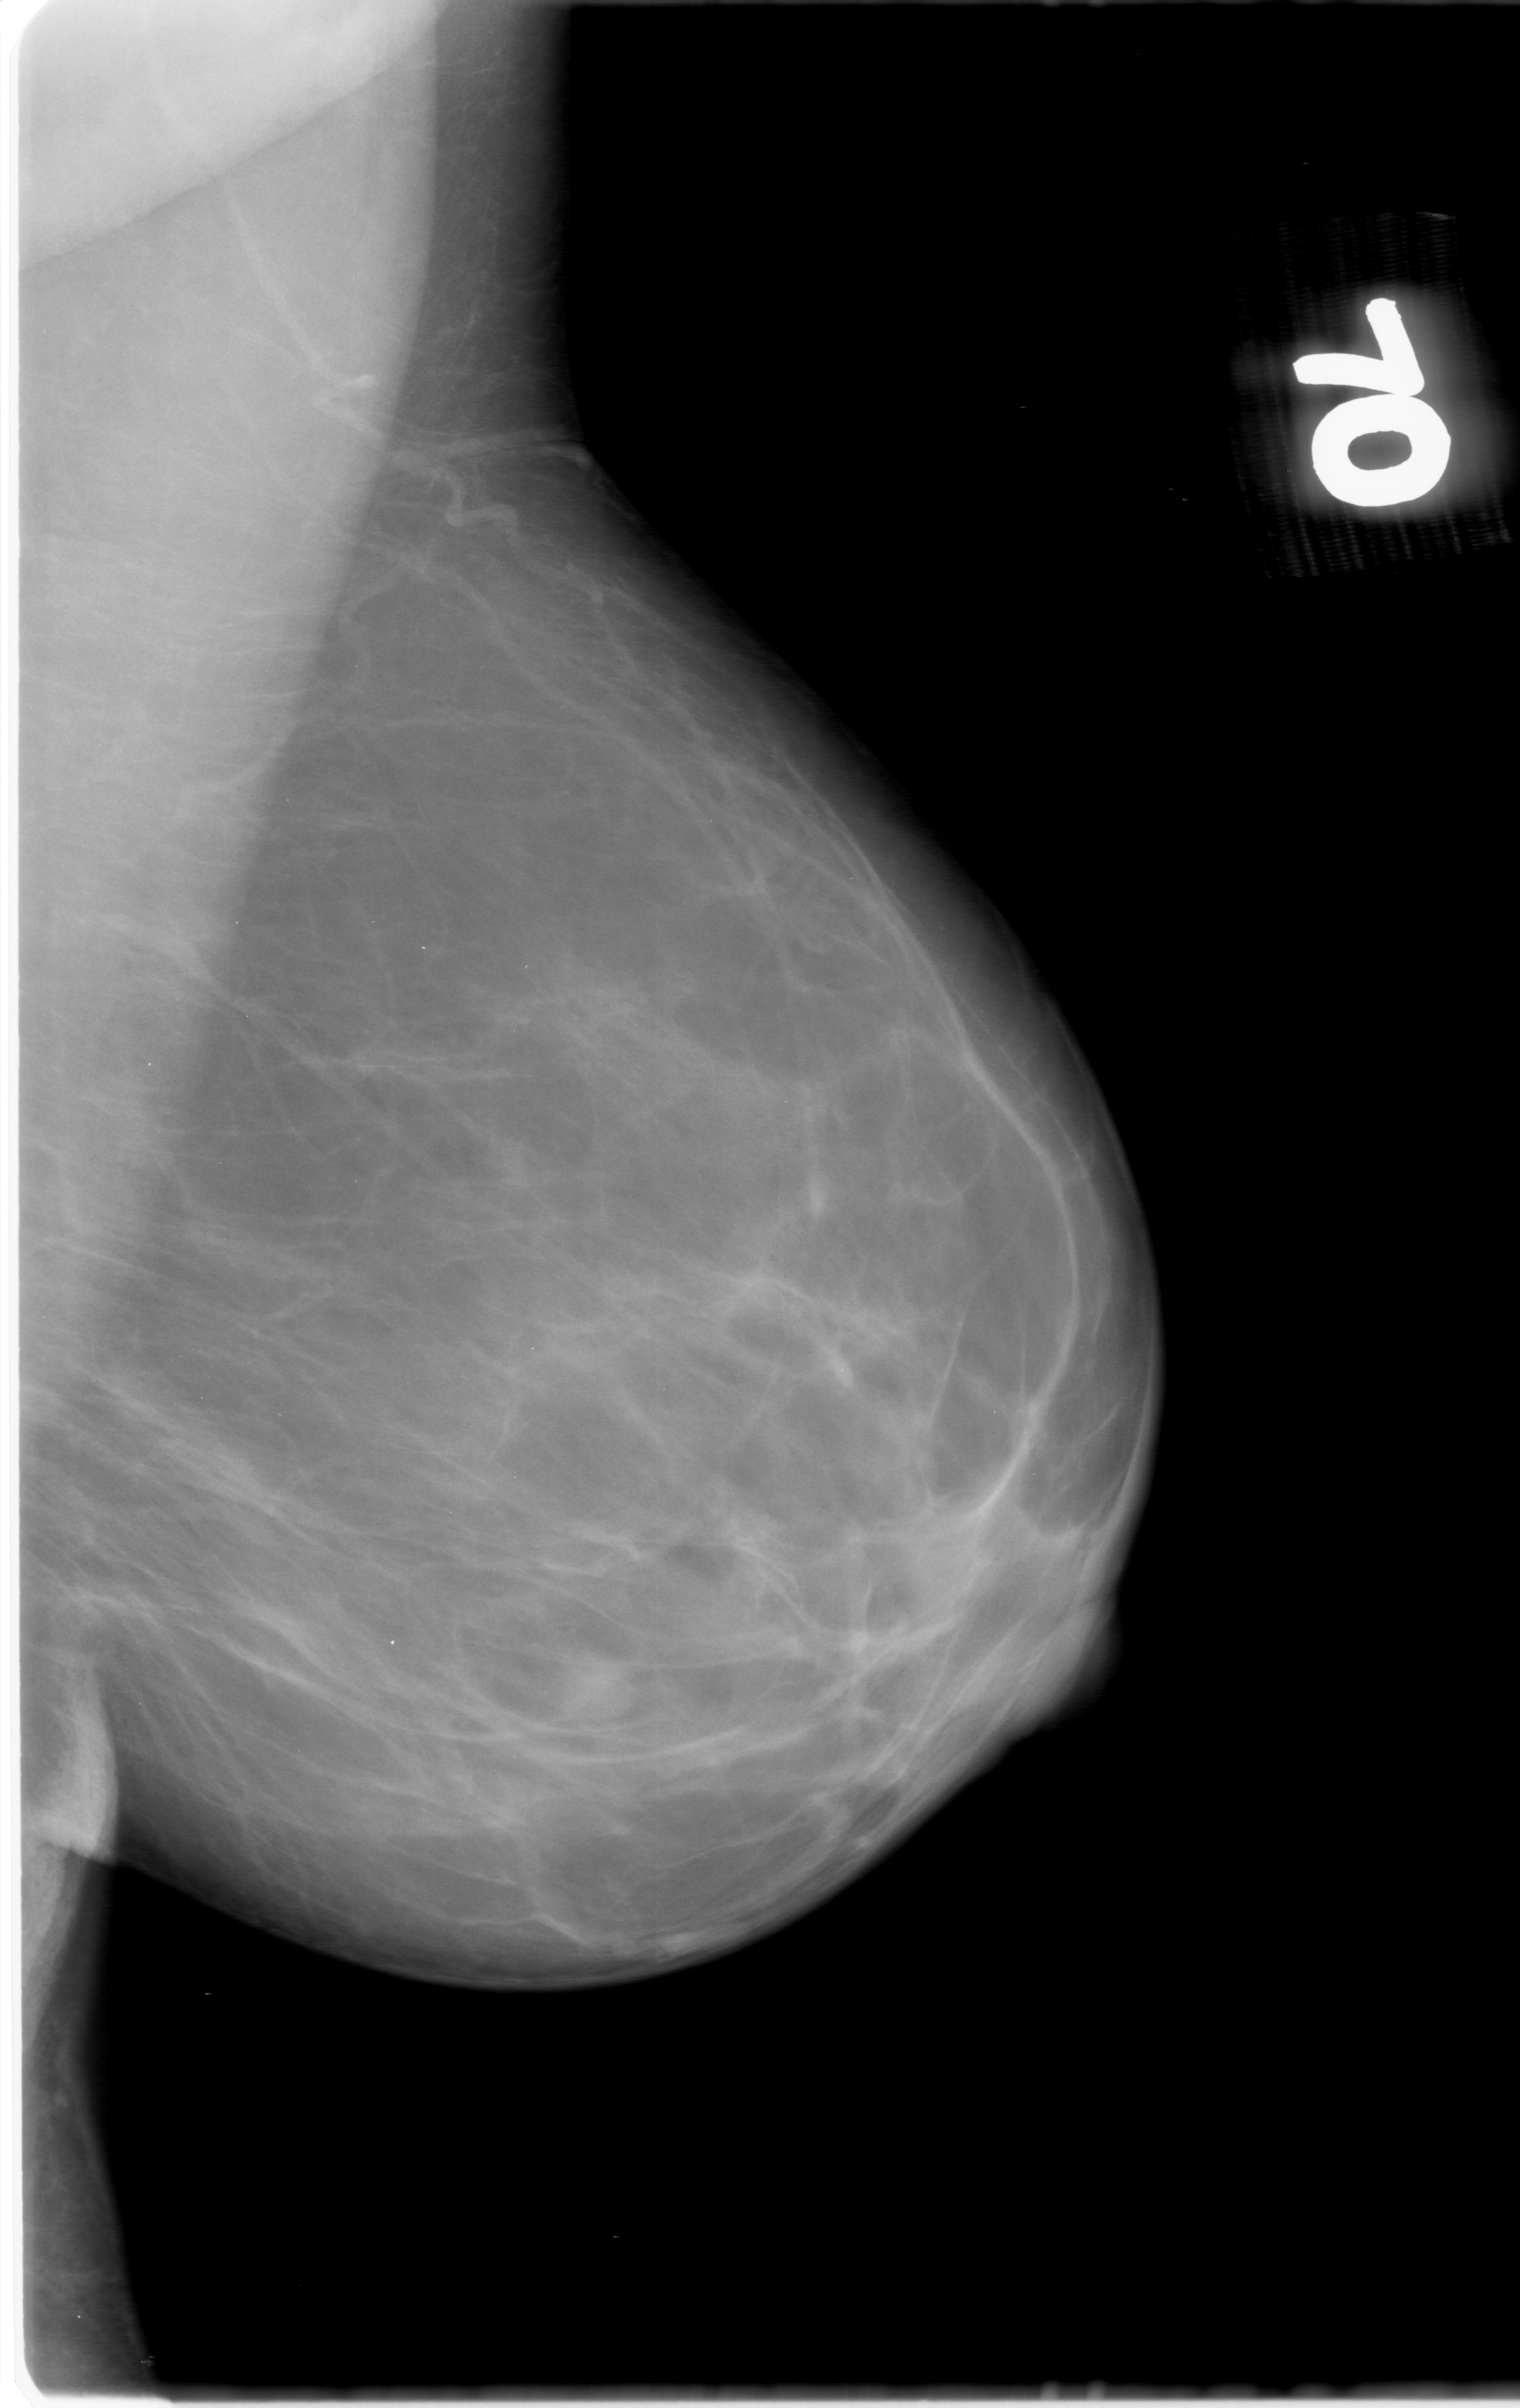
Scanned film-screen mammogram, left breast, mediolateral oblique (MLO) view, BI-RADS breast density category 1 (scale 1–4).
Radiologist-marked abnormalities on this image: mass, shape round, margins obscured; BI-RADS assessment category 0; subtlety rating 4 on a 1 (subtle) to 5 (obvious) scale; pathology result (as recorded, not read from the image): benign.